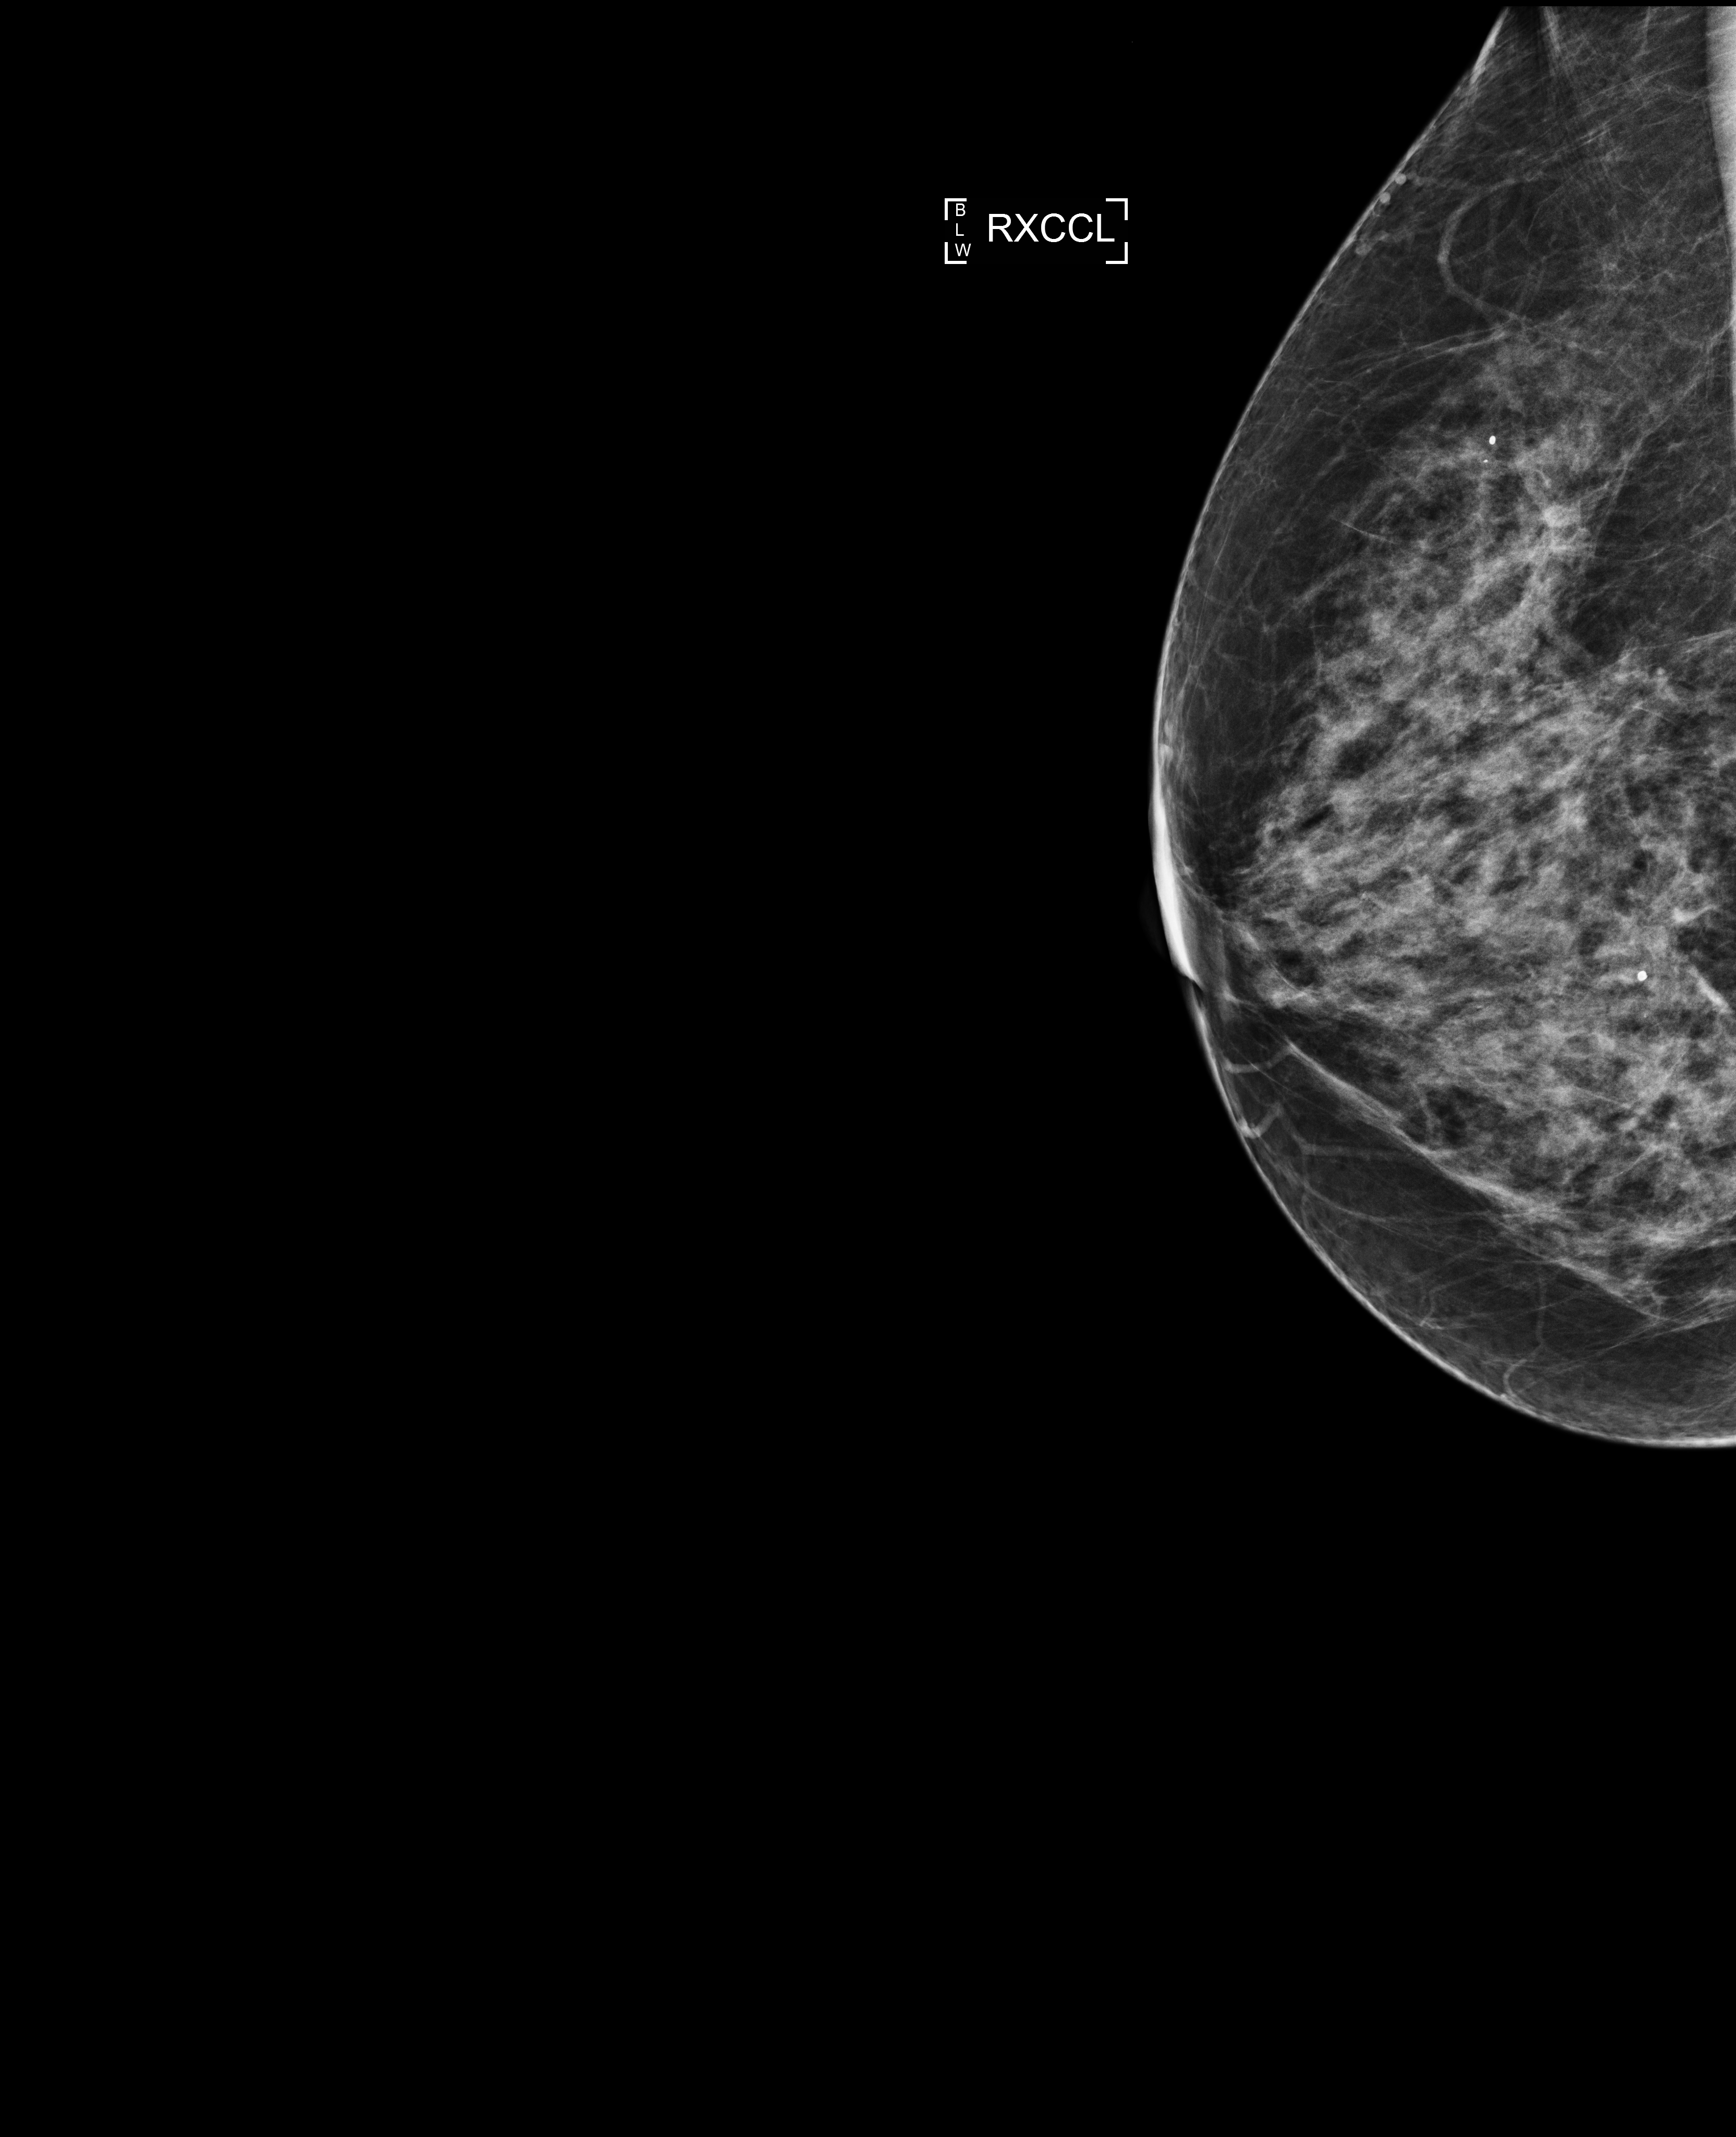
Digital mammogram (FFDM), right breast, exaggerated CC view (lateral), annual screening mammography examination, compressed breast thickness 62 mm. Female patient, age 60 years.
Breast density at the screening exam (both breasts): heterogeneously dense (BI-RADS density category c). Final BI-RADS category for the screening round (tomosynthesis exam, both breasts): category 2. Recall: no recall after this screen.